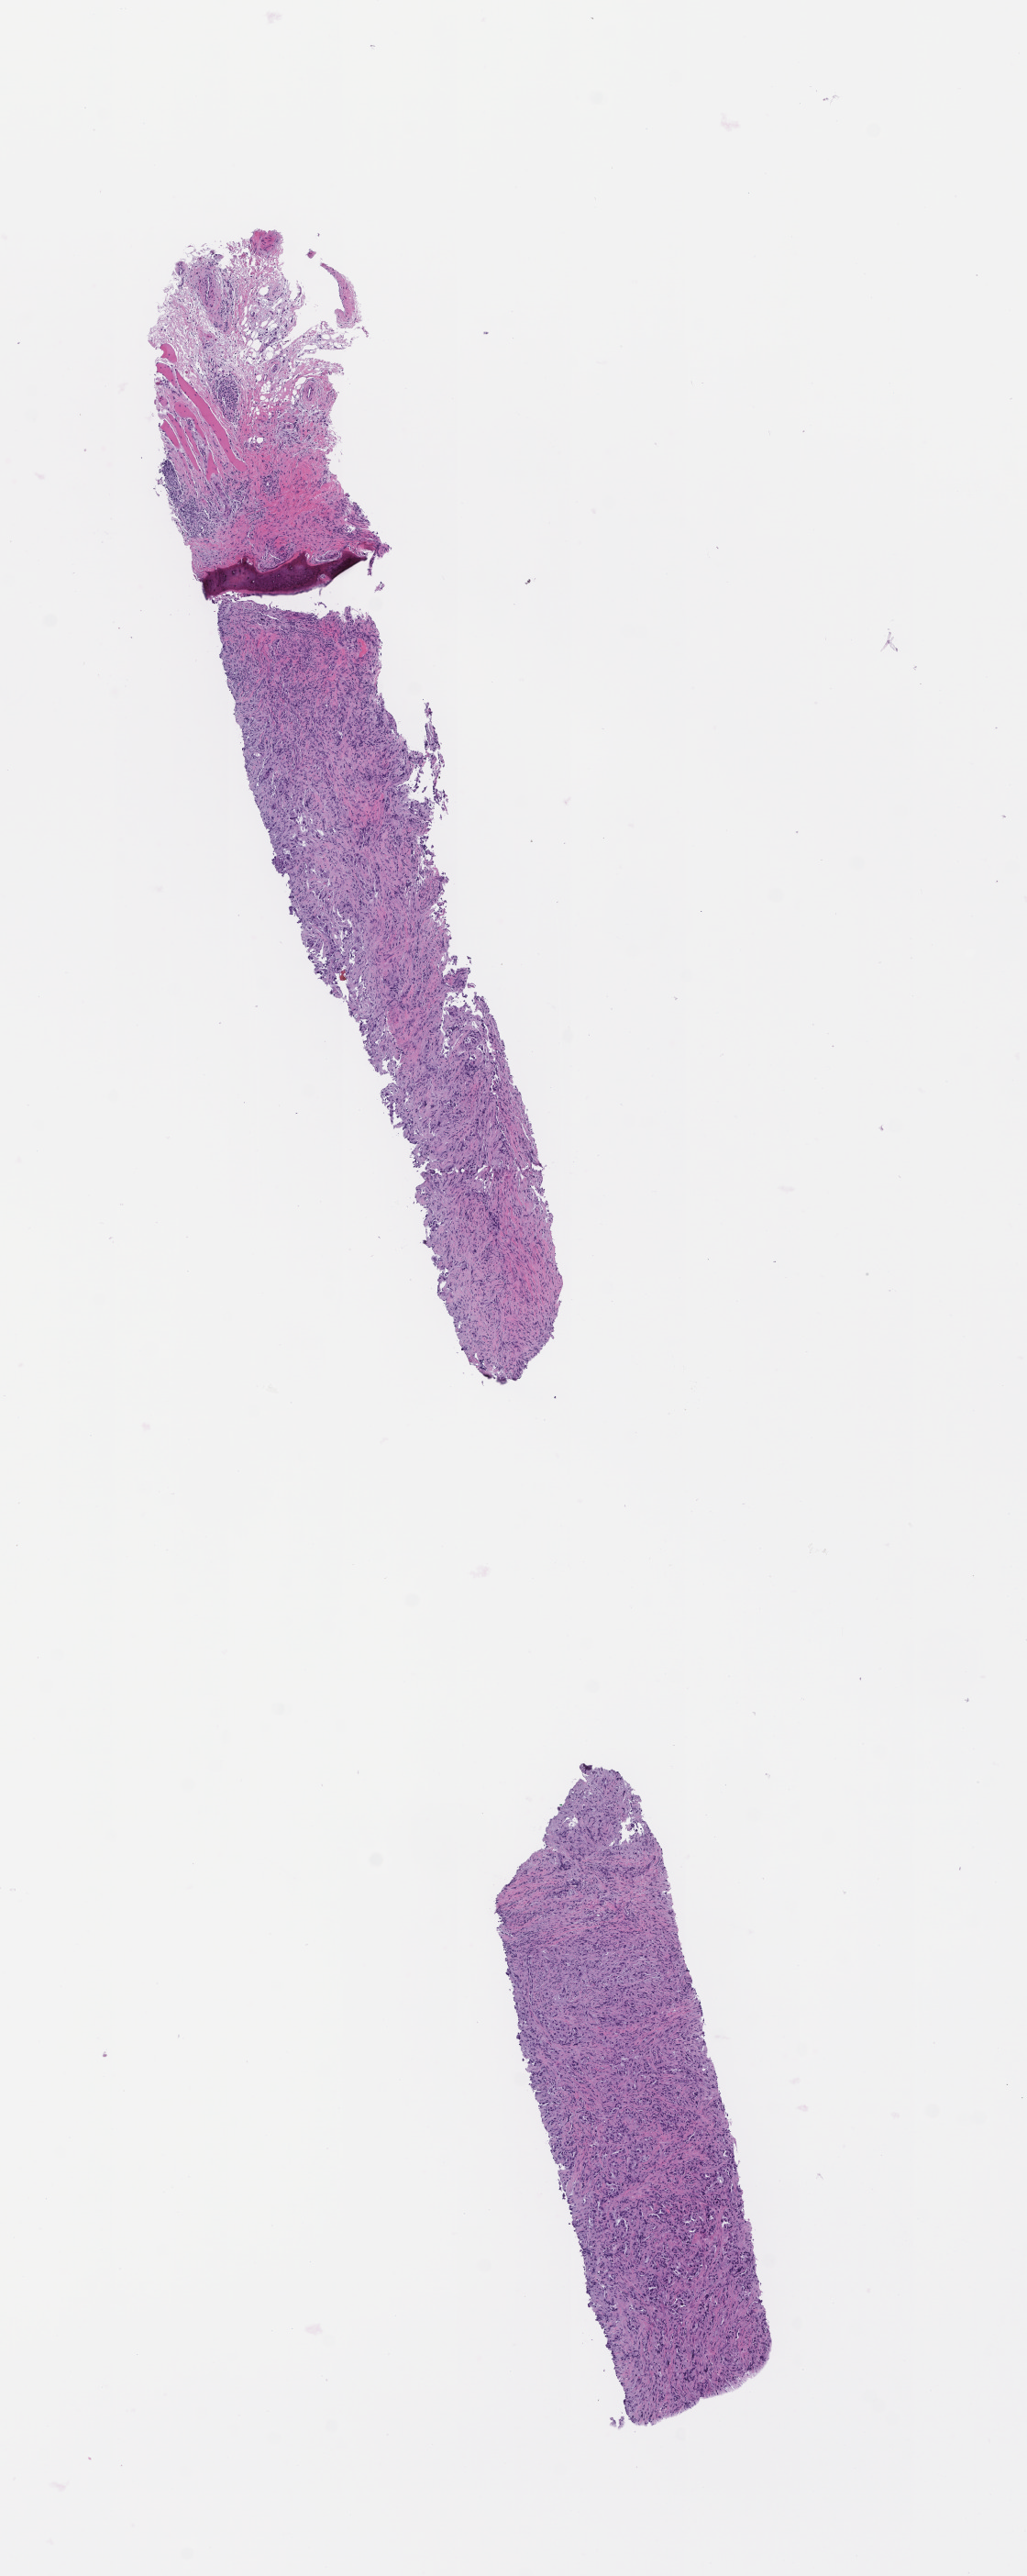
Whole-slide image, hematoxylin and eosin (H&E) stain — low-resolution overview of the scanned area, about 4.5 x 11.3 mm, formalin-fixed paraffin-embedded section, specimen time point: archival tissue. Patient sex: male.
This section: metastasis (sampled organ not recorded). Primary diagnosis of the patient: Non-Small Cell Lung Carcinoma.